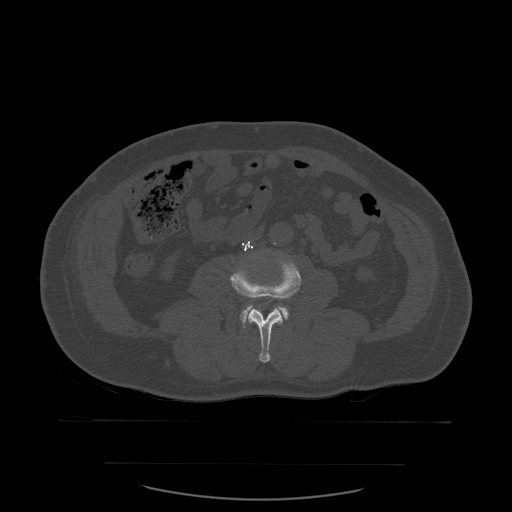
CT including the spine, one axial slice. Slice 184 of 590 in the series (ordered by position). Bone window (W 1800 / L 400 HU). 1.25 mm slice thickness. 512 × 512 image matrix. Patient age 71 years. From the clinical record (not read from this slice): primary cancer: lung; vertebrae with lytic lesions (as recorded): T1, T2, L5, S1.
Annotated regions visible in this slice (semi-automatic segmentation, software-assisted and operator-edited):
- L3 vertebra: bounding box (x1, y1, x2, y2) in pixels: (230, 253, 302, 363)
- L4 vertebra: (240, 305, 289, 324)